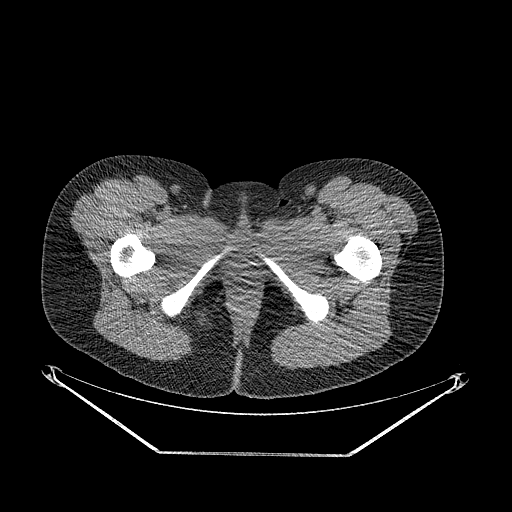
CT of an extremity soft-tissue mass (from a PET/CT study), one axial slice; slice 34 of 267 in the series (ordered by position); soft-tissue window (W 400 / L 40 HU); 3.75 mm slice thickness; 512 × 512 image matrix. Female patient. Case-level facts recorded for this patient, not image findings: histological type: epithelioid sarcoma; grade: intermediate; site of the primary tumour: right buttock.
Annotated regions visible in this slice (expert contour drawn on MRI and transferred to this co-registered scan by the dataset authors):
- gross tumour volume including surrounding oedema: bounding box (x1, y1, x2, y2) in pixels: (180, 297, 220, 343)
- gross tumour volume (mass): (185, 304, 211, 334)